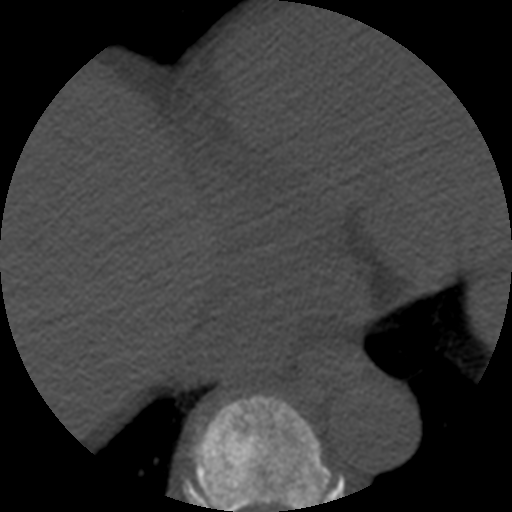
CT including the spine, one axial slice. Slice 305 of 508 in the series (ordered by position). Reconstruction kernel STANDARD. Bone window (W 1800 / L 400 HU). 1.25 mm slice thickness. 512 × 512 image matrix, field of view 160 × 160 mm. Patient age 57 years. From the clinical record (not read from this slice): primary cancer: prostate.
Structures marked on this image (semi-automatically segmented with operator editing):
- T8 vertebra: bounding box [x1, y1, x2, y2] px = [189, 393, 331, 512]